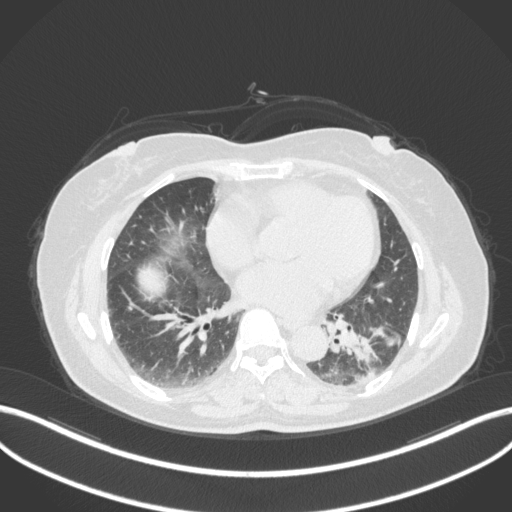
Chest CT, one axial slice. Position 159 of 307 along the scan axis. 120 kVp. Lung window (W 1500 / L -600 HU). 512 × 512 image matrix. Patient: female, 59 years. Case-level facts recorded for this patient, not image findings: clinical TNM (as recorded): T2a N0 M0; histopathological grade: G2-3.
Structures marked on this image (bounding box drawn by a radiologist):
- lung tumour (recorded histology: adenocarcinoma): bounding box (x1, y1, x2, y2) in pixels: (324, 326, 387, 385)